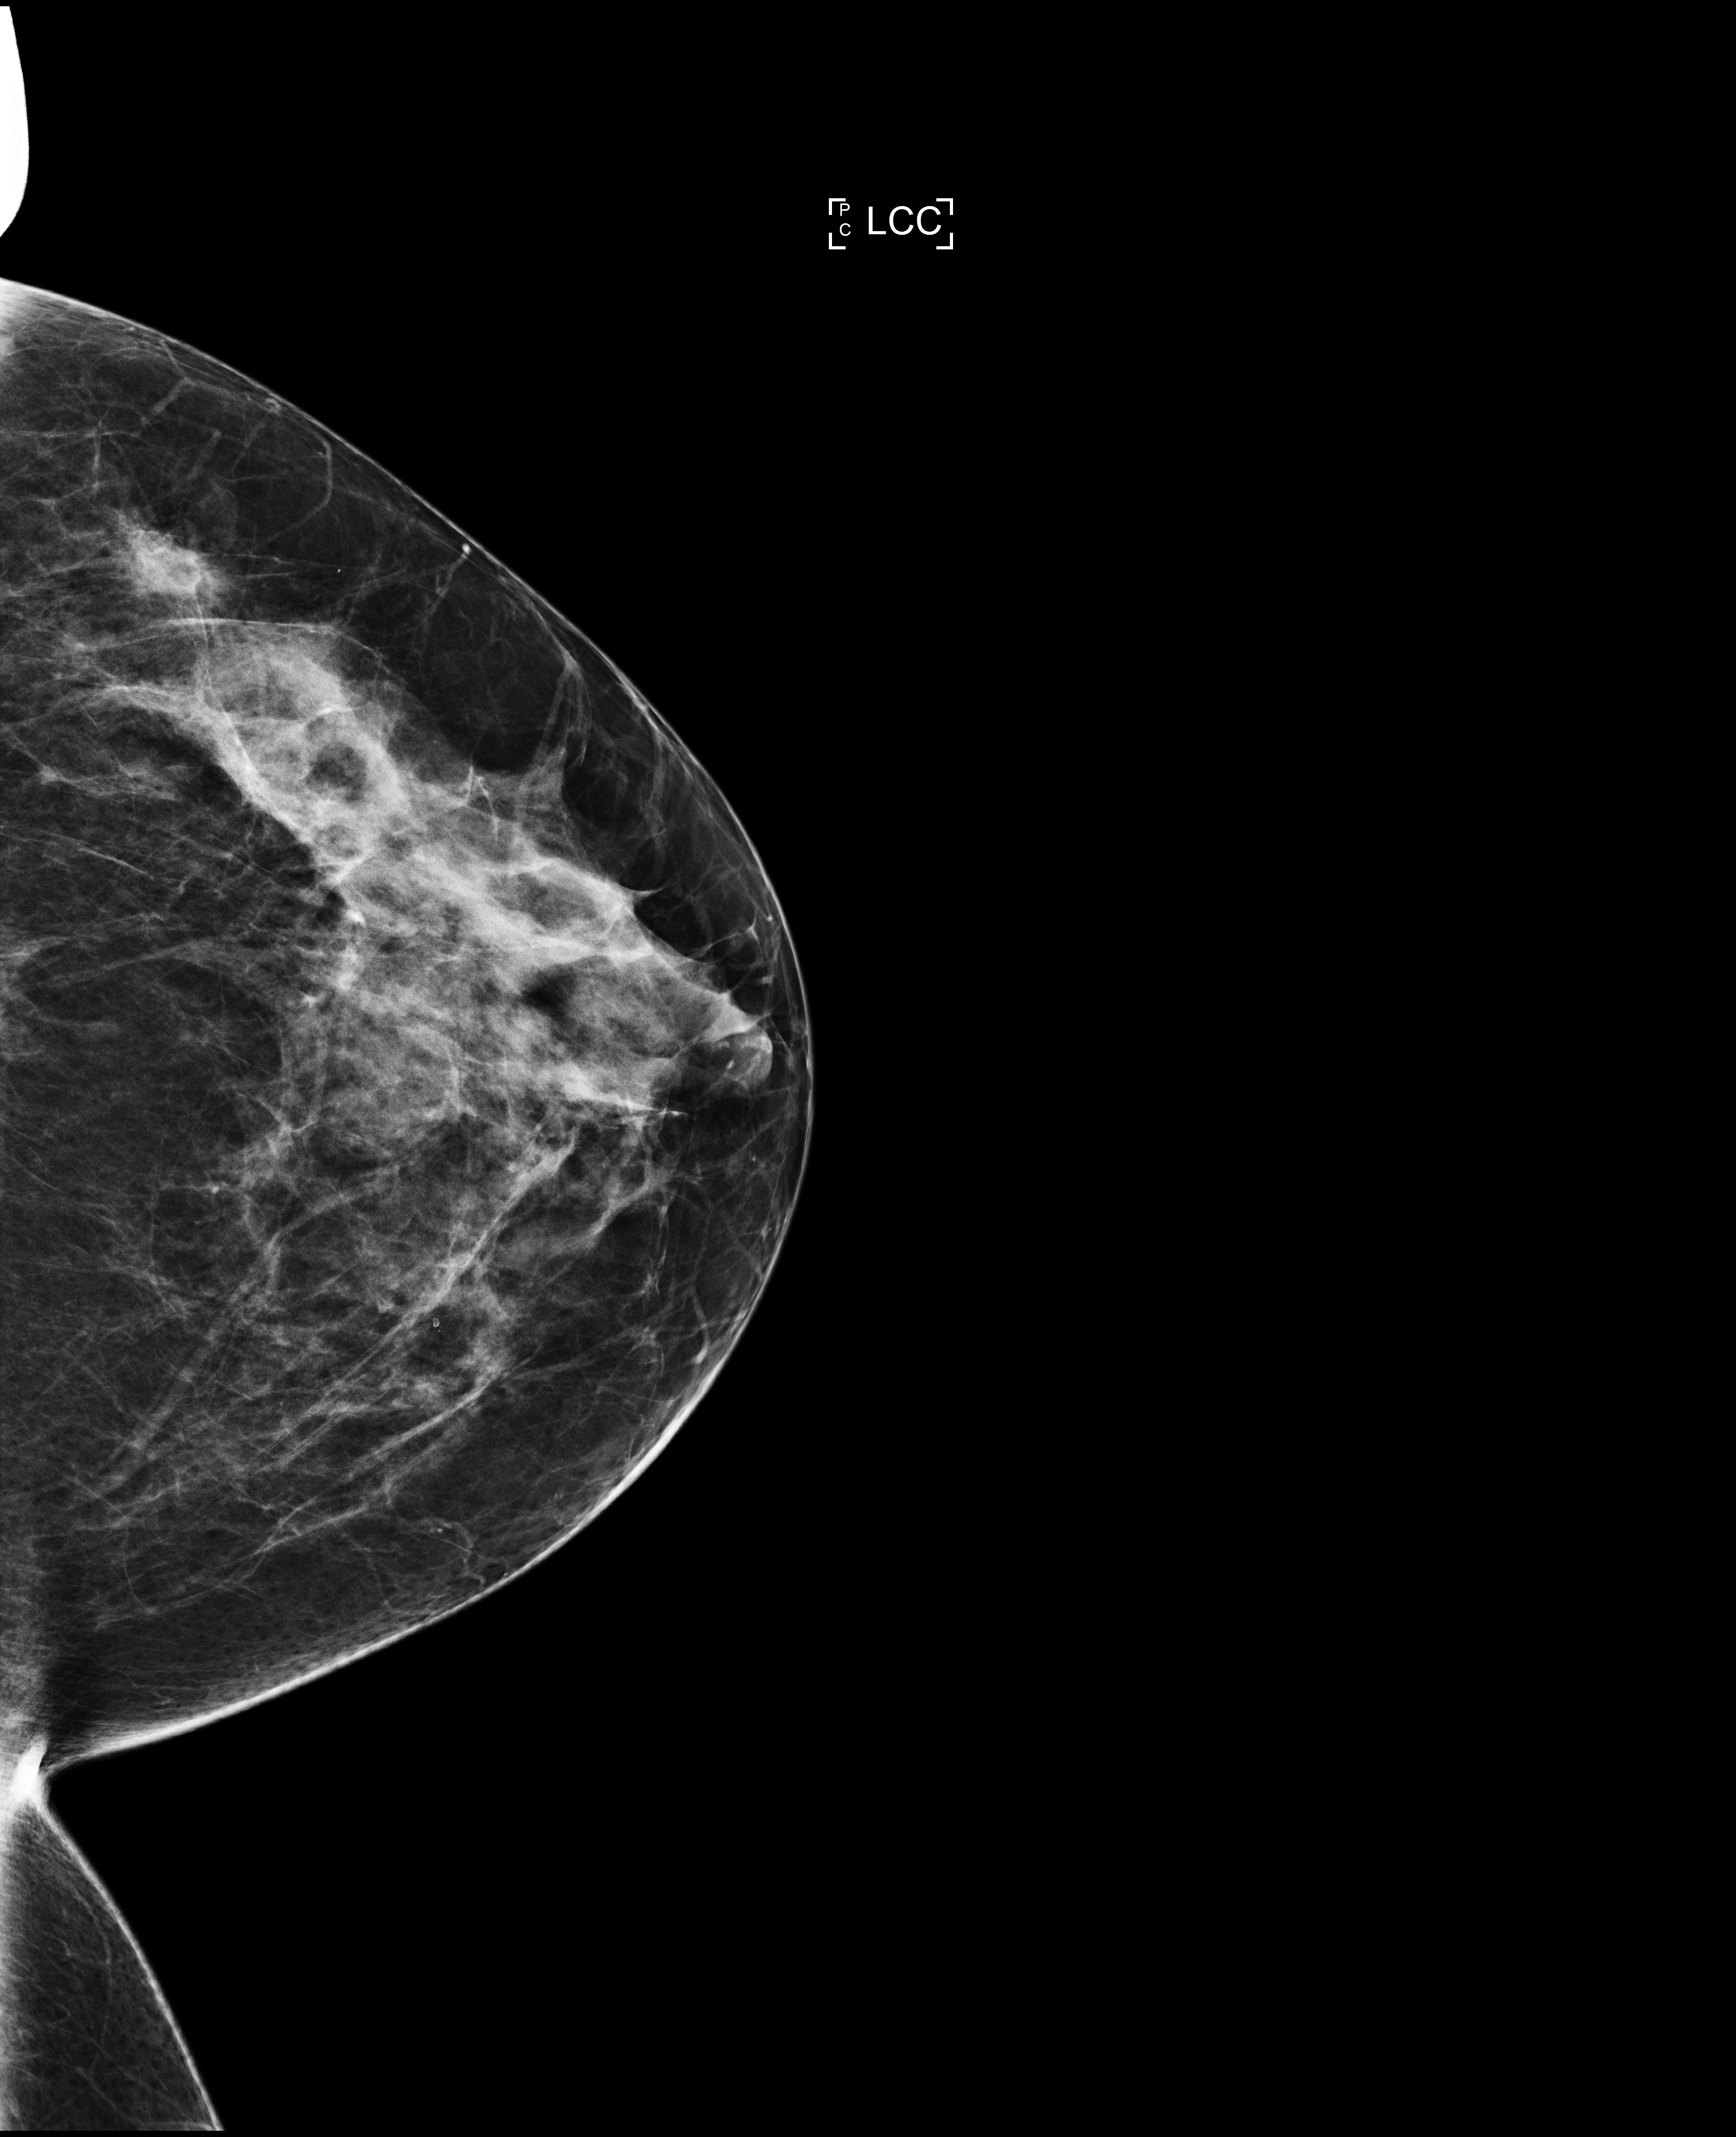
Annual screening mammography examination; compressed breast thickness 58 mm. Female patient, age 49 years.
Image type: full-field digital mammogram. Breast: left. Projection: craniocaudal (CC) view.